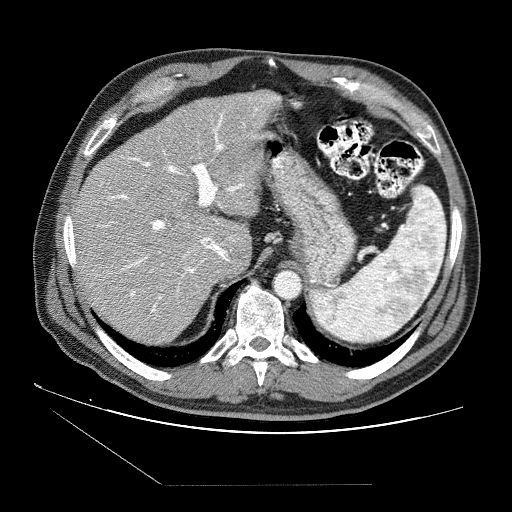
Contrast-enhanced abdominal CT (liver protocol), one axial slice; position 58 of 87 along the scan axis; reconstruction kernel STANDARD; soft-tissue window (W 400 / L 40 HU); 2.5 mm slice thickness; 512 × 512 image matrix, field of view 400 × 400 mm. From the clinical record (not read from this slice): diagnosis: hepatocellular carcinoma (patient treated with transarterial chemoembolisation; whether this scan precedes or follows treatment is not stated here); TNM stage (as recorded): Stage-II; Child-Pugh class: B; tumour differentiation: no biopsy; tumour nodularity: multinodular.
Structures marked on this image (semi-automatically segmented with operator editing):
- liver parenchyma outside the tumour (the mass and vessels are separate outlines, so this box may not span the whole liver): bounding box [x1, y1, x2, y2] px = [73, 90, 282, 342]
- liver vessels: [78, 97, 280, 313]